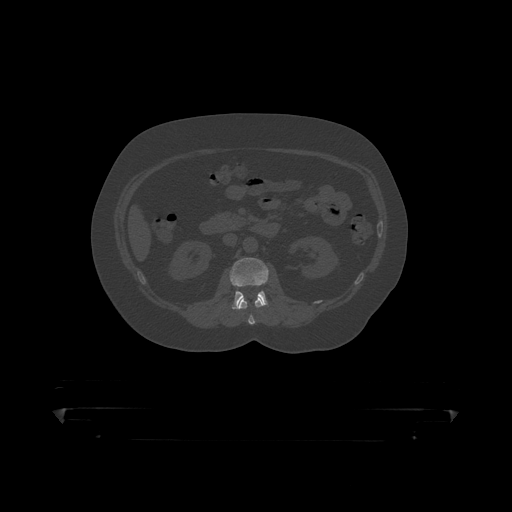
CT including the spine, one axial slice. Position 129 of 390 along the scan axis. Reconstruction kernel STANDARD. 120 kVp. Bone window (W 1800 / L 400 HU). 512 × 512 image matrix, field of view 650 × 650 mm. Male patient, age 60 years. From the clinical record (not read from this slice): primary cancer: prostate.
Outlined on this slice (semi-automatic segmentation, software-assisted and operator-edited):
- L1 vertebra: bounding box (x1, y1, x2, y2) in pixels: (239, 299, 265, 319)
- L2 vertebra: (230, 258, 269, 310)